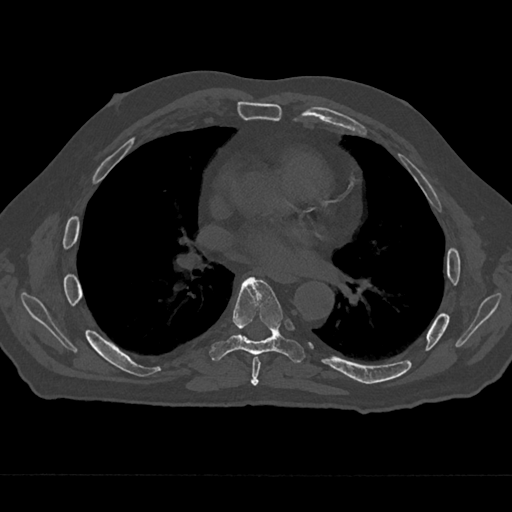
CT including the spine, one axial slice; slice 376 of 797 in the series (ordered by position); reconstruction kernel Br40s/3; 120 kVp; bone window (W 1800 / L 400 HU); 0.5 mm slice thickness; 512 × 512 image matrix, field of view 377 × 377 mm. Male patient, age 75 years. From the clinical record (not read from this slice): primary cancer: renal.
Structures marked on this image (semi-automatic segmentation, software-assisted and operator-edited):
- T6 vertebra: bounding box (x1, y1, x2, y2) in pixels: (251, 356, 261, 386)
- T7 vertebra: (209, 277, 305, 363)